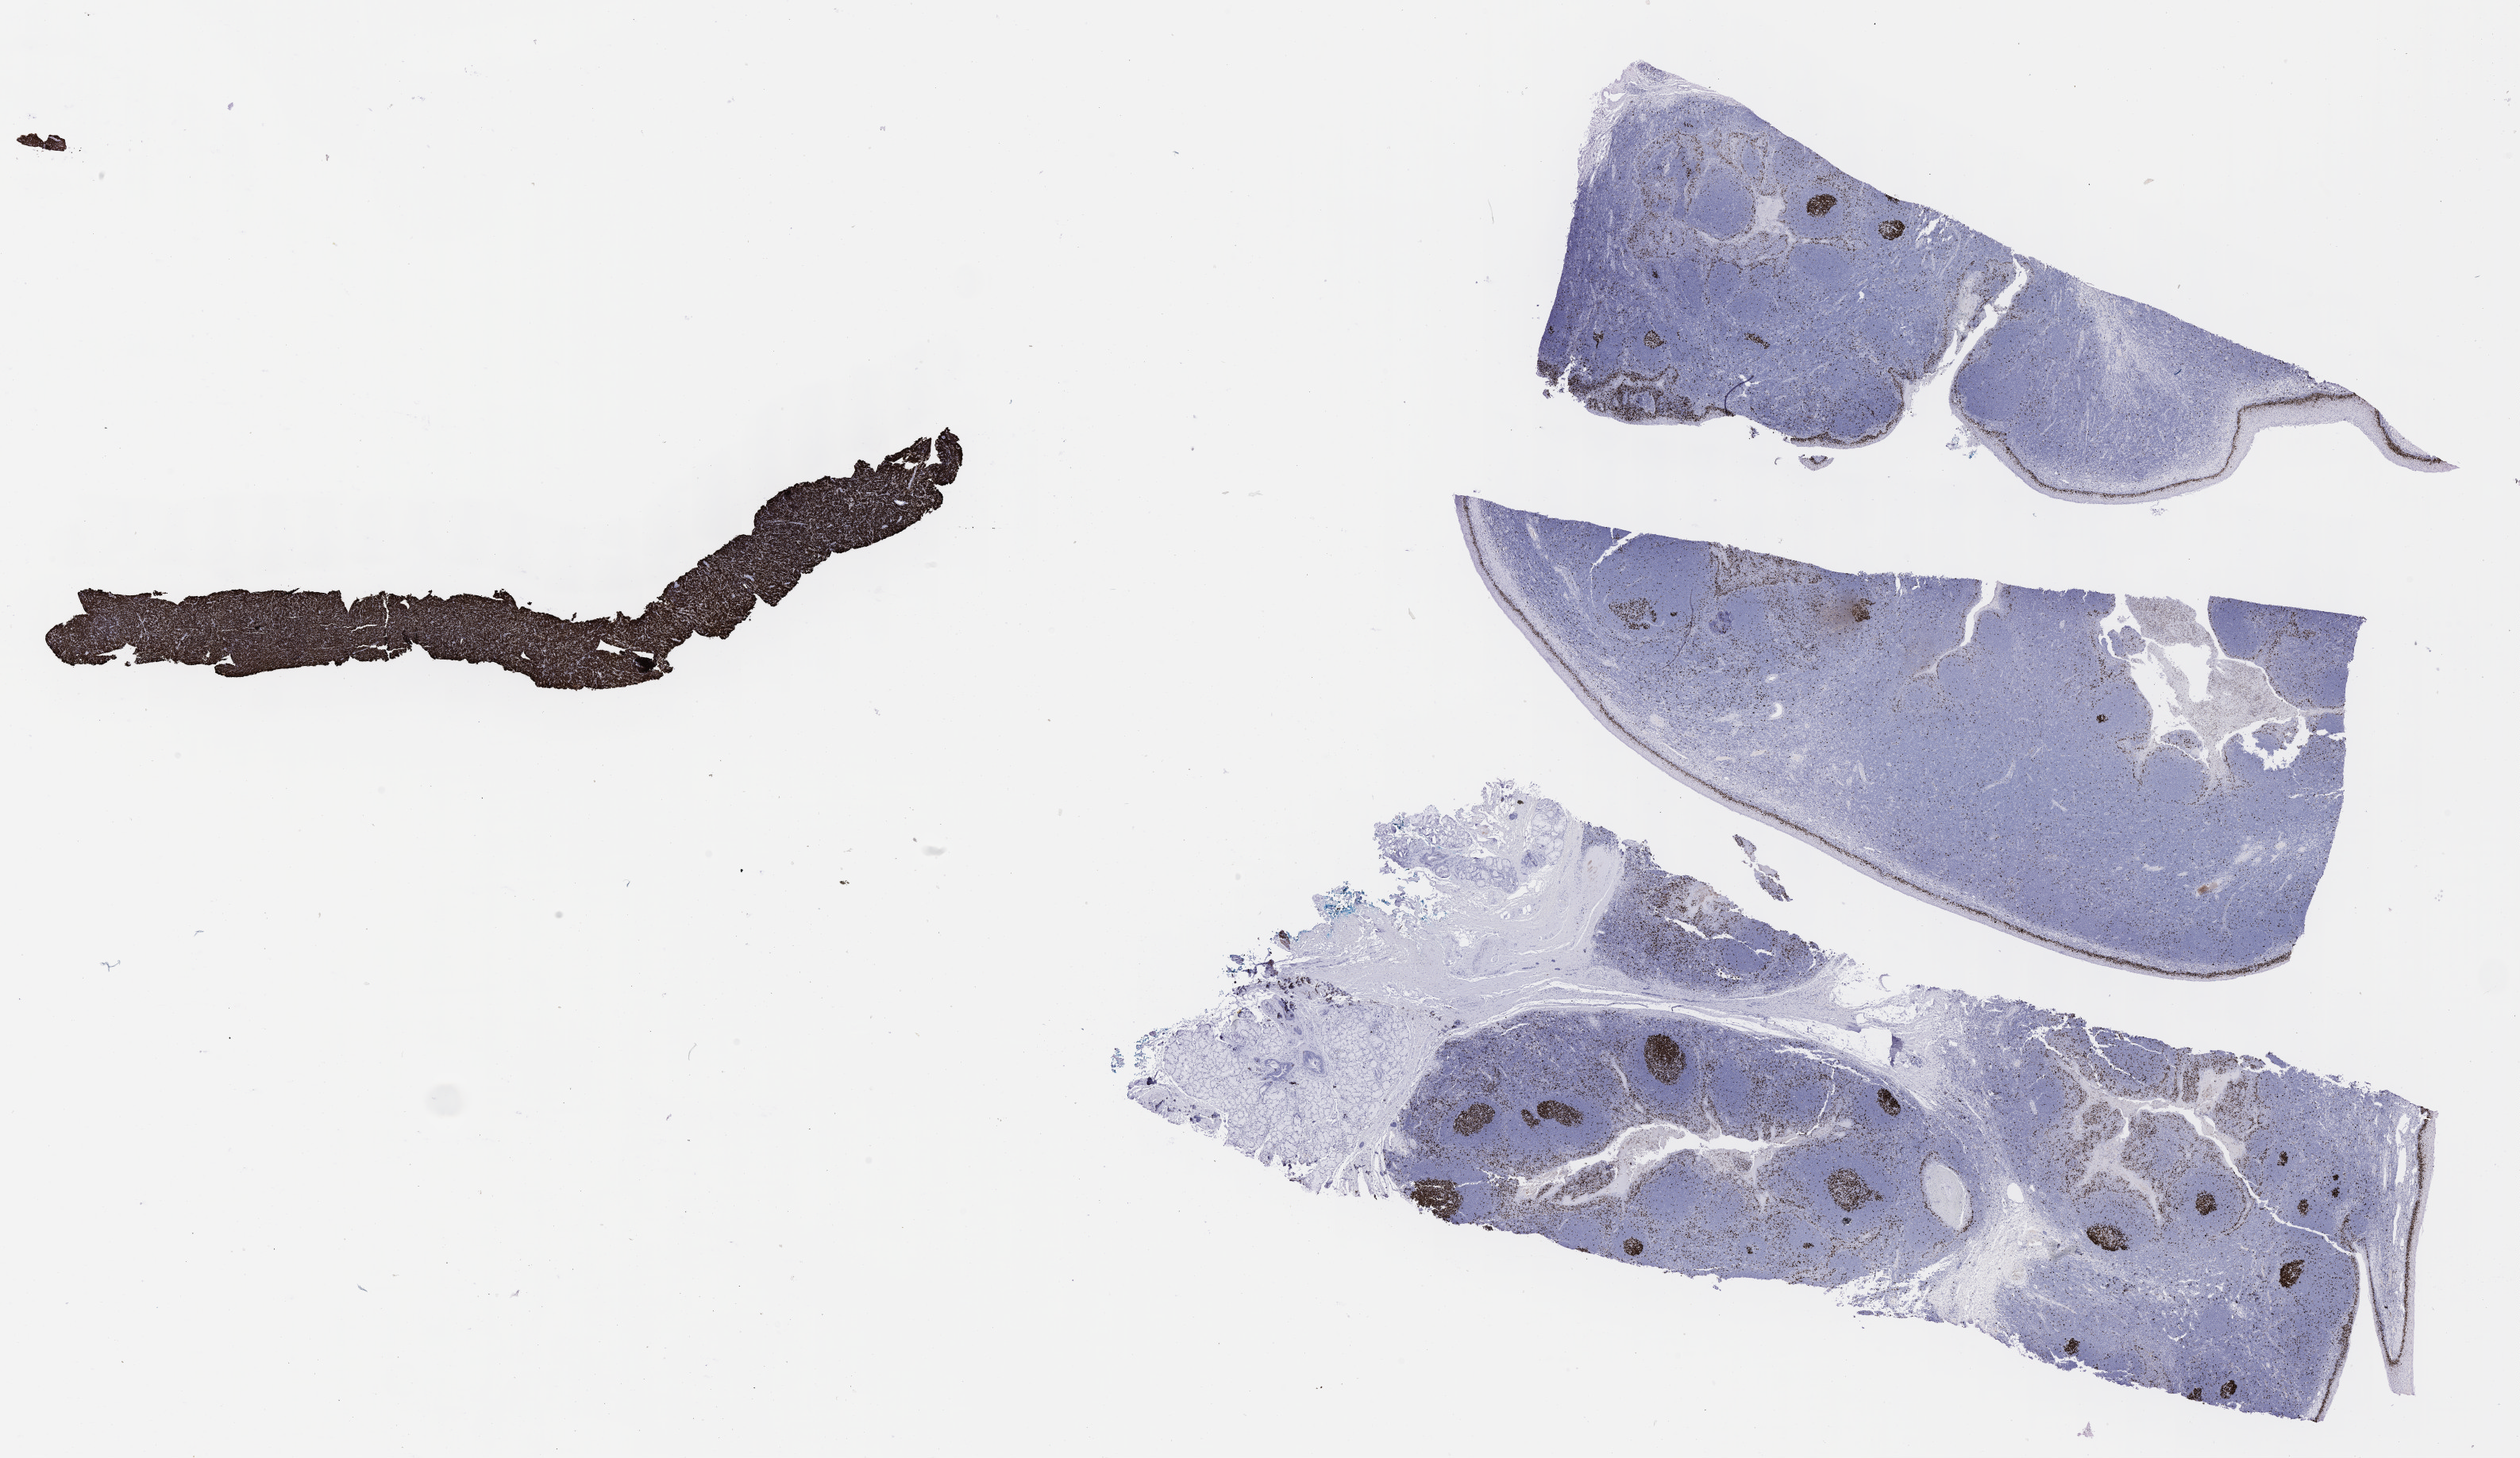
IHC for Ki-67, whole-slide image, shown as a low-resolution overview of the whole scanned area (about 25.7 x 14.9 mm). Tumor tissue. Site: kidney. Male, age 9 years at initial diagnosis.
- histologic diagnosis: Burkitt lymphoma, NOS